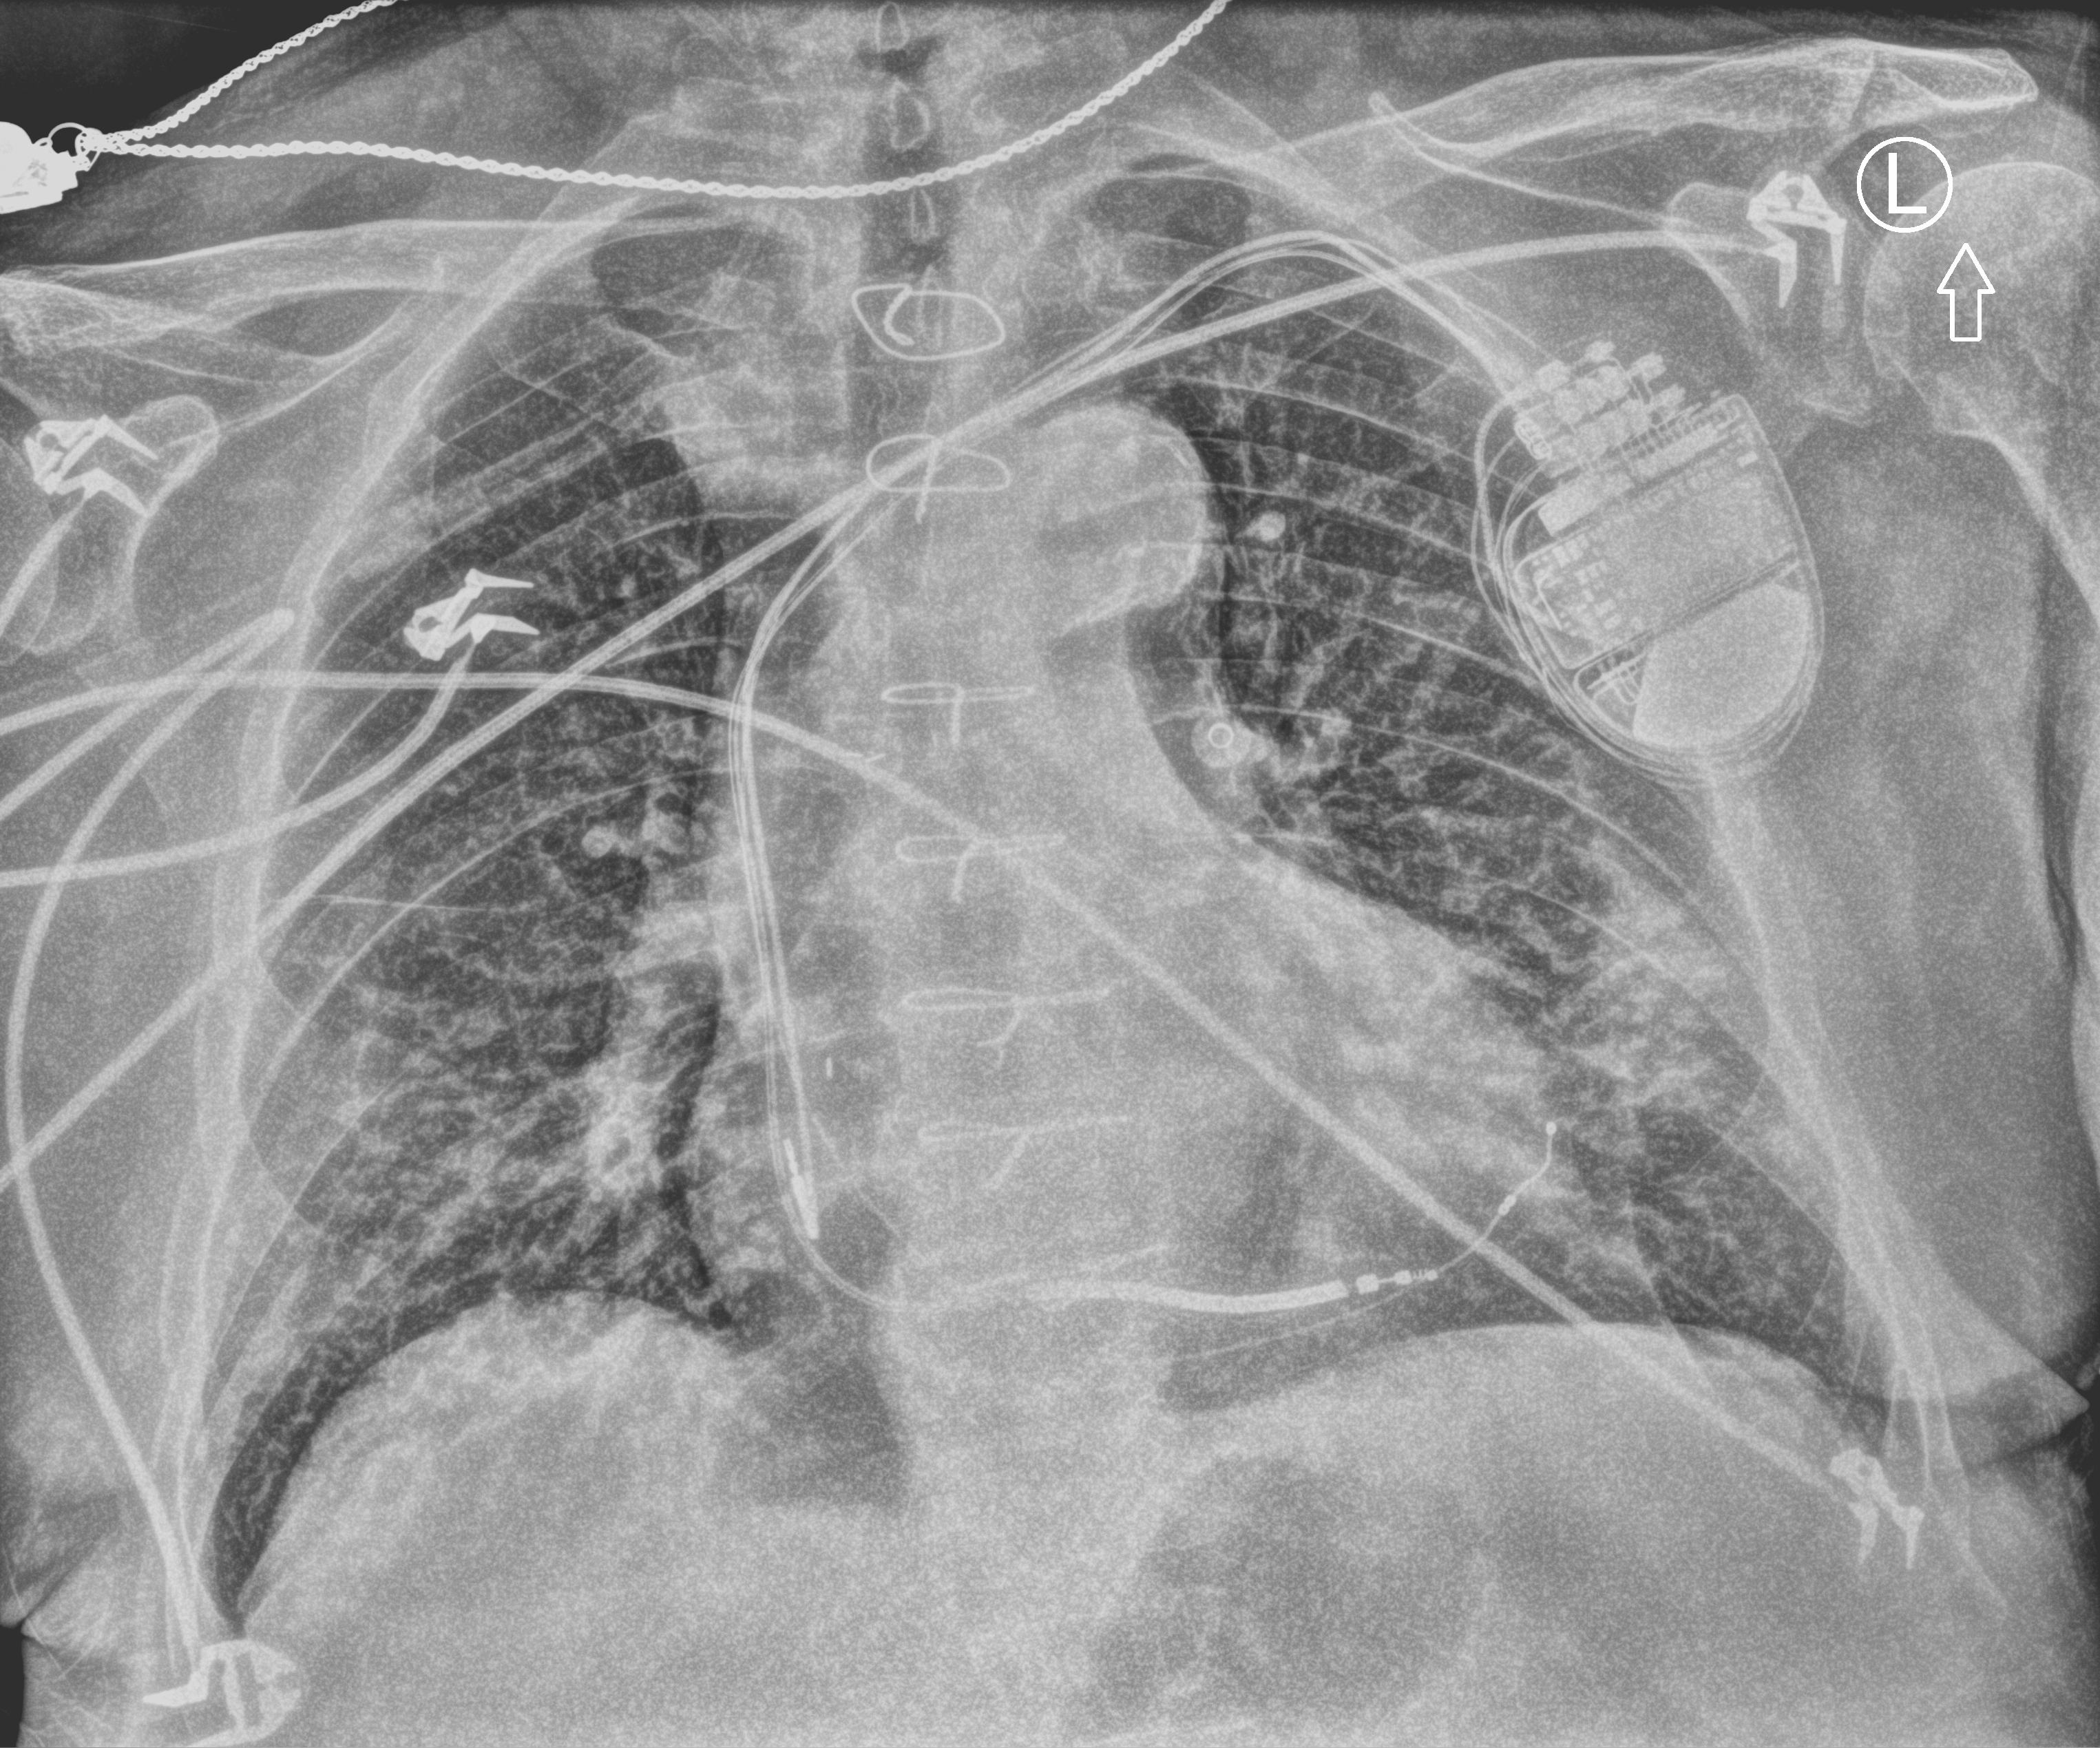
Bedside chest radiograph (computed radiography); anteroposterior (AP) projection. Male patient hospitalised with COVID-19, age 75–90 years.
Admission-level facts for this patient (not findings on this image; timing relative to this image not recorded):
- mechanically ventilated during this hospital stay: no